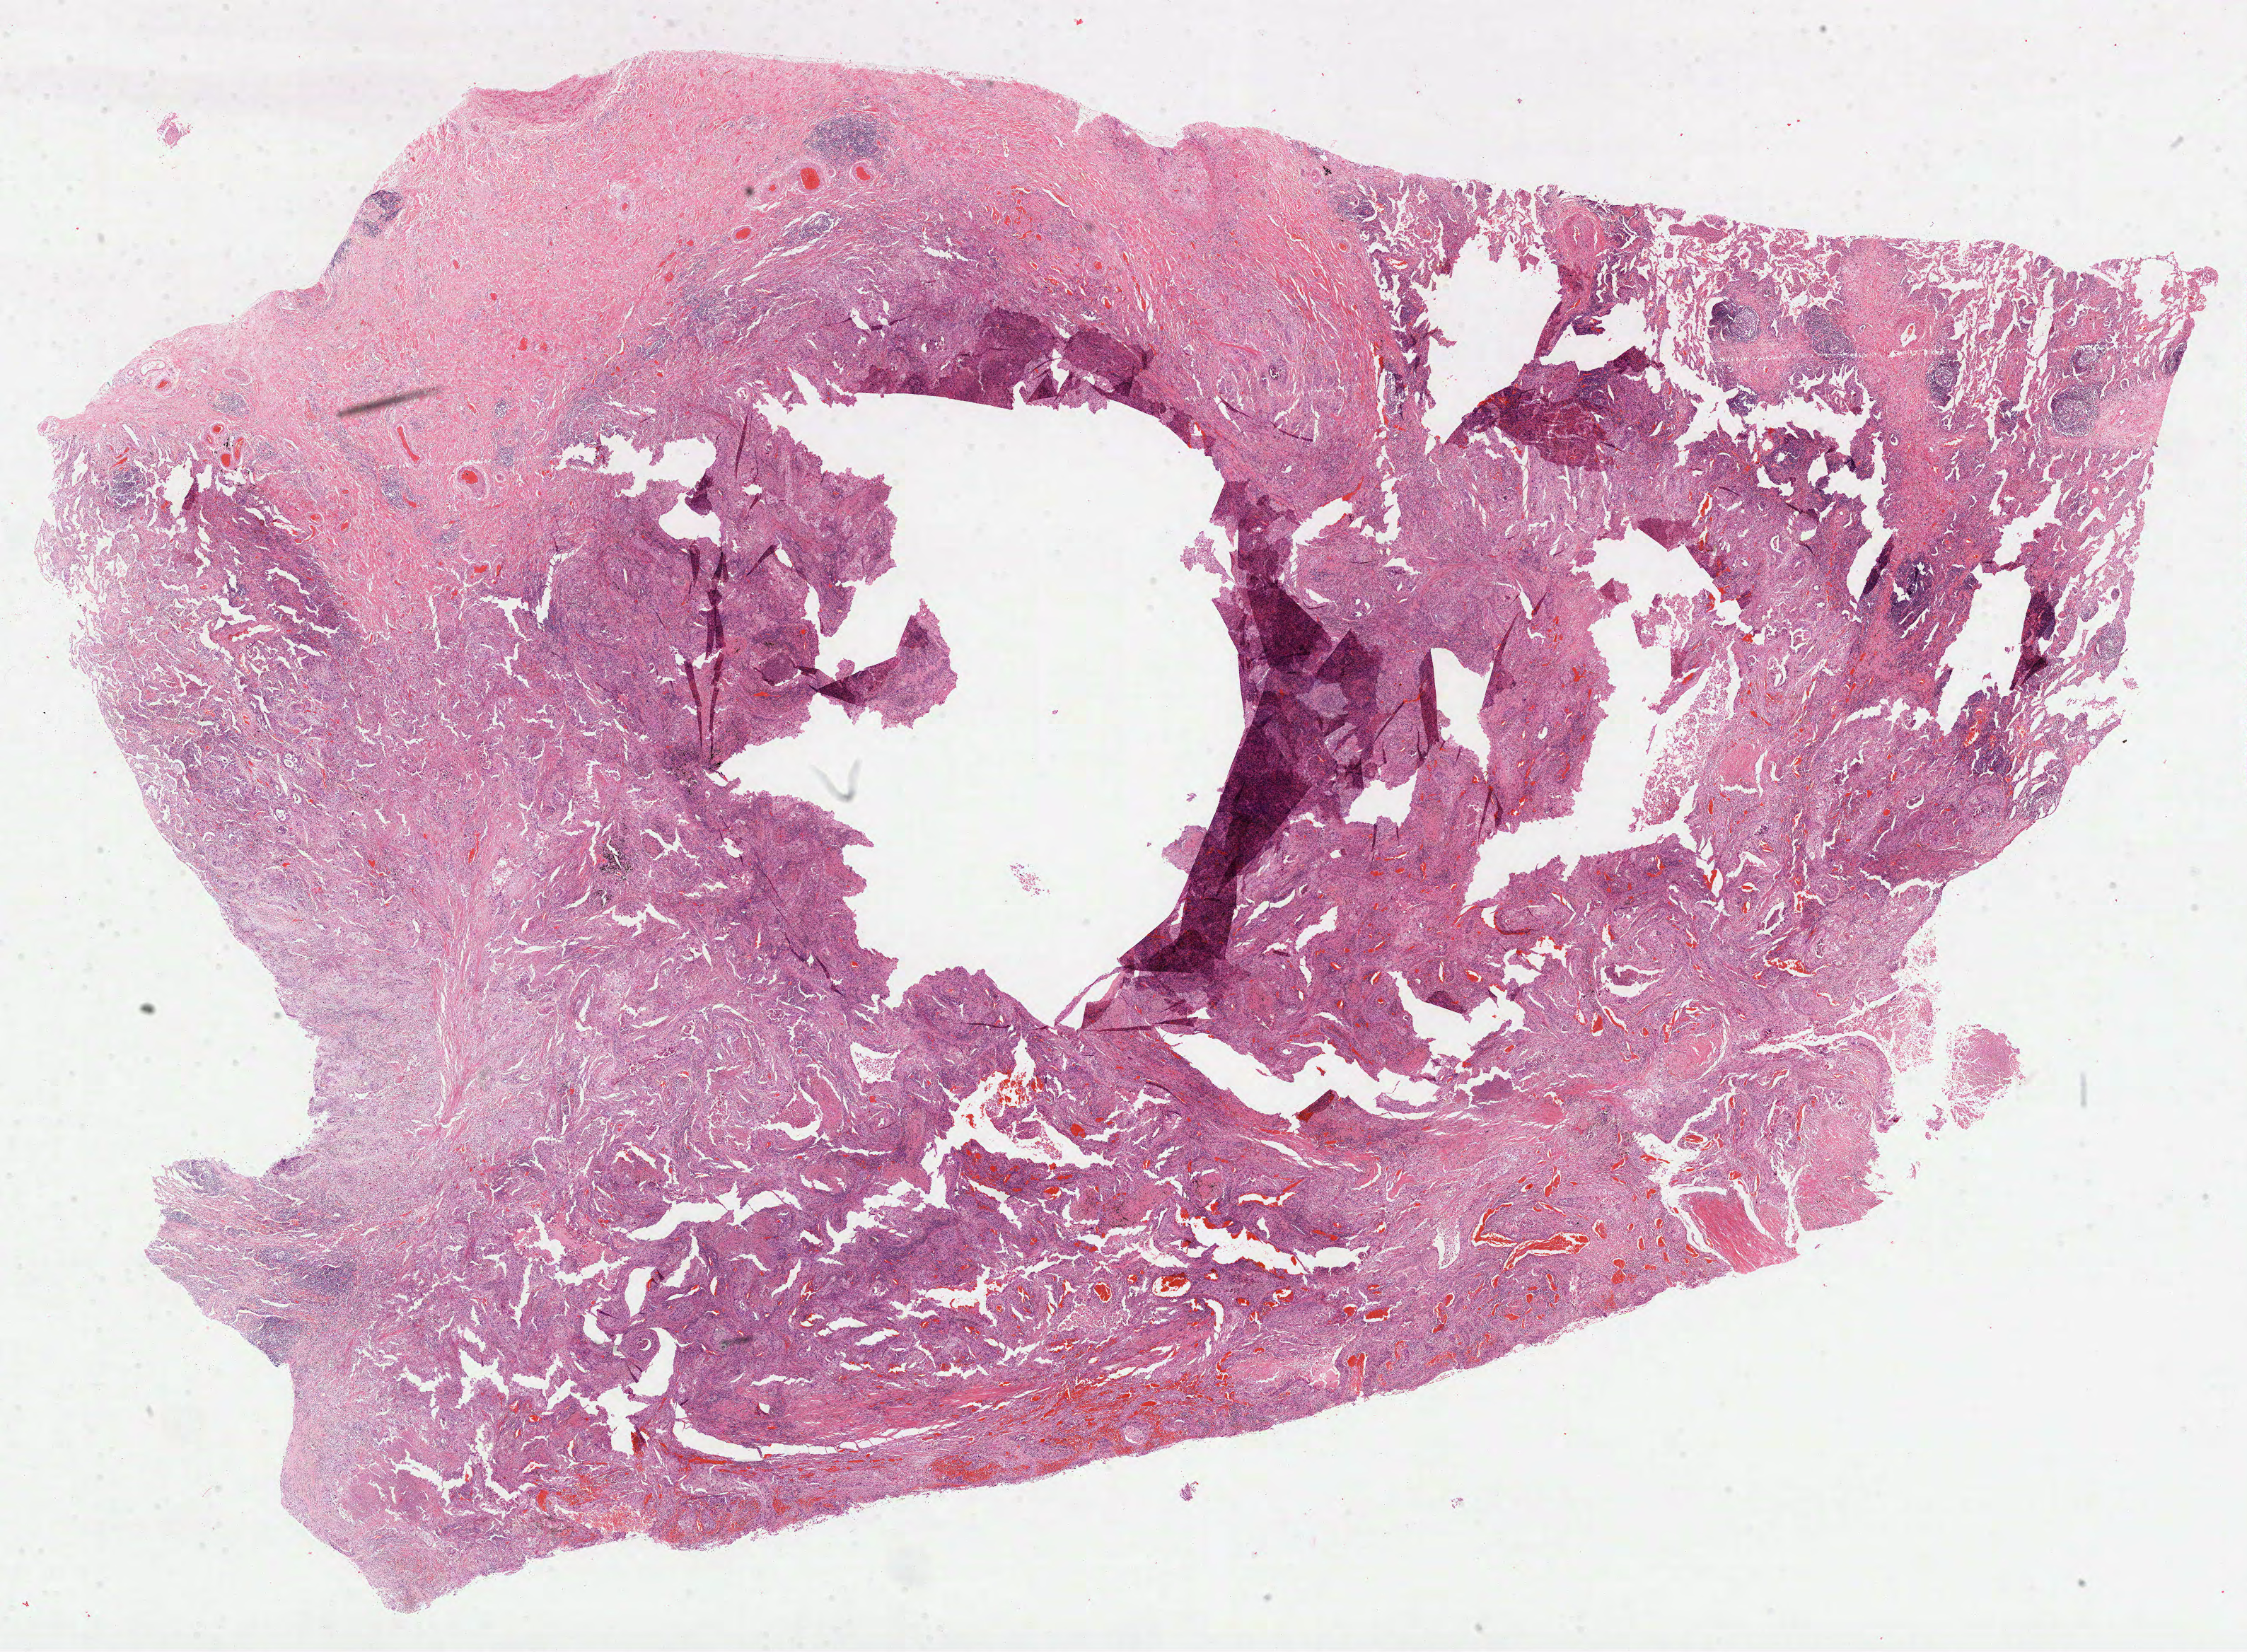
Digitized Hematoxylin and eosin (H&E) stained tissue section (whole slide) — a low-resolution overview of the entire scanned area, about 25.6 x 18.8 mm (from a 40x scan); formalin-fixed paraffin-embedded (FFPE) diagnostic section; primary tumour sample from the lung. Male, age 70 years at initial diagnosis.
Pathologic diagnosis: Squamous cell carcinoma, NOS (upper lobe, lung). AJCC pathologic stage: IIB. Laterality: left.